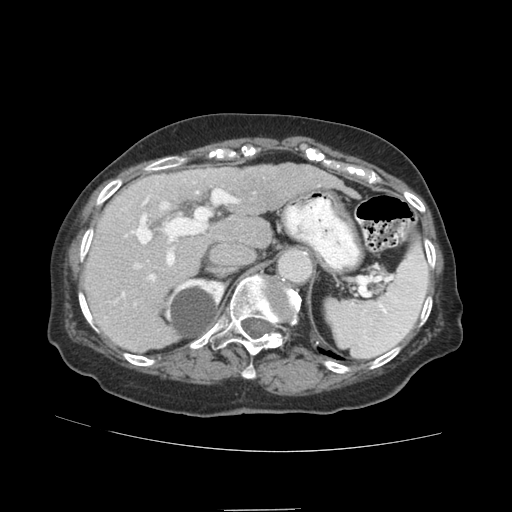
Contrast-enhanced abdominal CT (liver protocol), one axial slice; position 59 of 89 along the scan axis; reconstruction kernel STANDARD; 140 kVp; soft-tissue window (W 400 / L 40 HU); 512 × 512 image matrix, field of view 360 × 360 mm. From the clinical record (not read from this slice): diagnosis: hepatocellular carcinoma (patient treated with transarterial chemoembolisation; whether this scan precedes or follows treatment is not stated here); TNM stage (as recorded): Stage-II; Child-Pugh class: A; tumour differentiation: moderately differentiated; tumour nodularity: multinodular.
Outlined on this slice (semi-automatically segmented with operator editing):
- liver parenchyma outside the tumour (the mass and vessels are separate outlines, so this box may not span the whole liver): bounding box [x1, y1, x2, y2] px = [84, 164, 328, 350]
- mass: [233, 166, 285, 214]
- liver vessels: [105, 173, 320, 318]